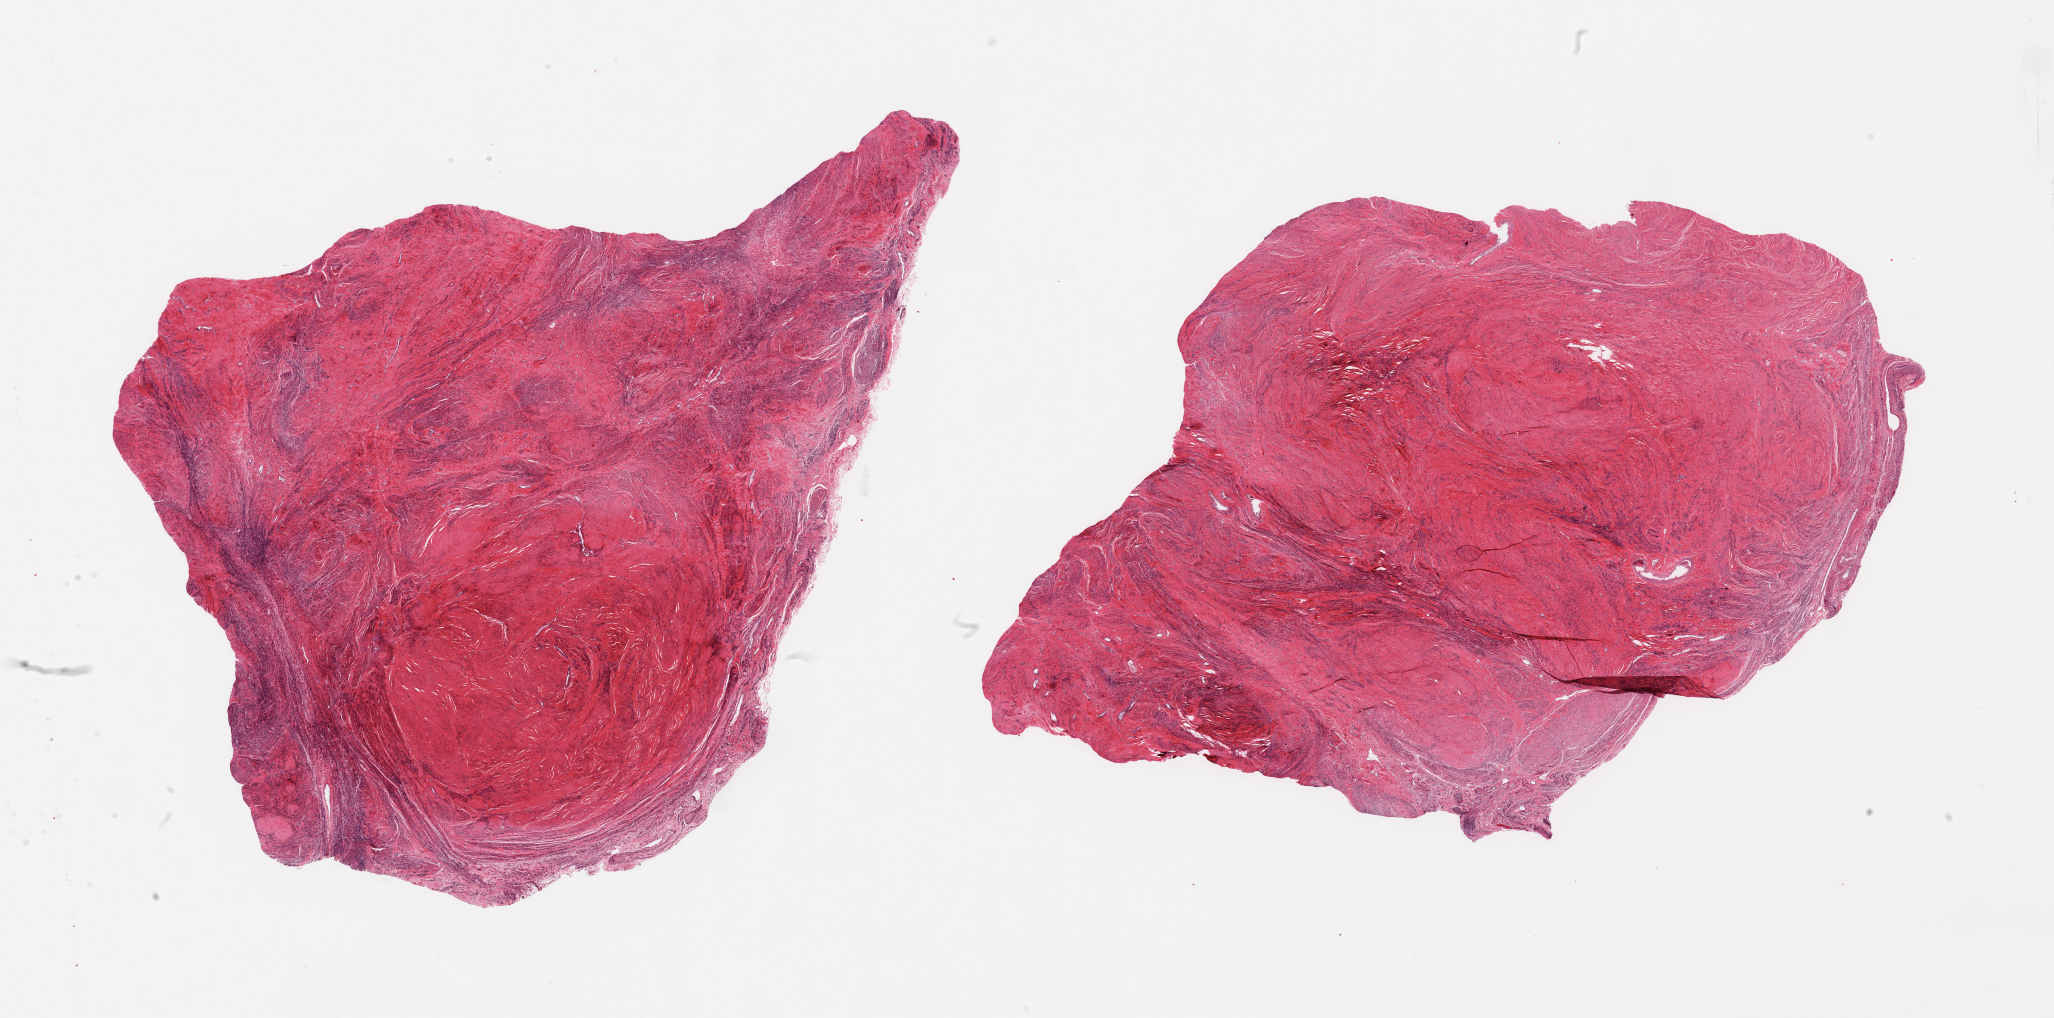
Digitized haematoxylin and eosin-stained section, brightfield, shown as a low-resolution overview of the whole scanned area (about 32.5 x 16.1 mm, slide scanned at 20x), PAXgene-fixed paraffin-embedded (PFPE) section, section of ovary (target tissue), donor tissue sample.
Reviewer comment on this tissue sample: 2 pieces, post menopausal atrophy; incidental ~5mm fibroma noted.